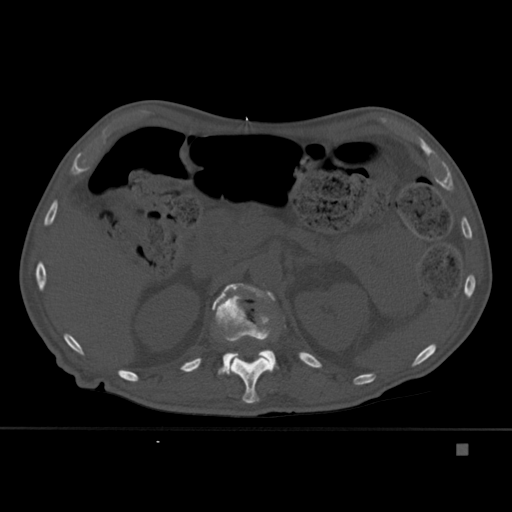
CT including the spine, one axial slice. Slice 193 of 451 in the series (ordered by position). Bone window (W 1800 / L 400 HU). 1.5 mm slice thickness. 512 × 512 image matrix. Male patient, age 75 years. From the clinical record (not read from this slice): primary cancer: prostate.
Annotated regions visible in this slice (semi-automatic segmentation, software-assisted and operator-edited):
- L1 vertebra: bounding box <212,283,279,375> (left, top, right, bottom; pixels)
- T12 vertebra: <230,313,286,404>